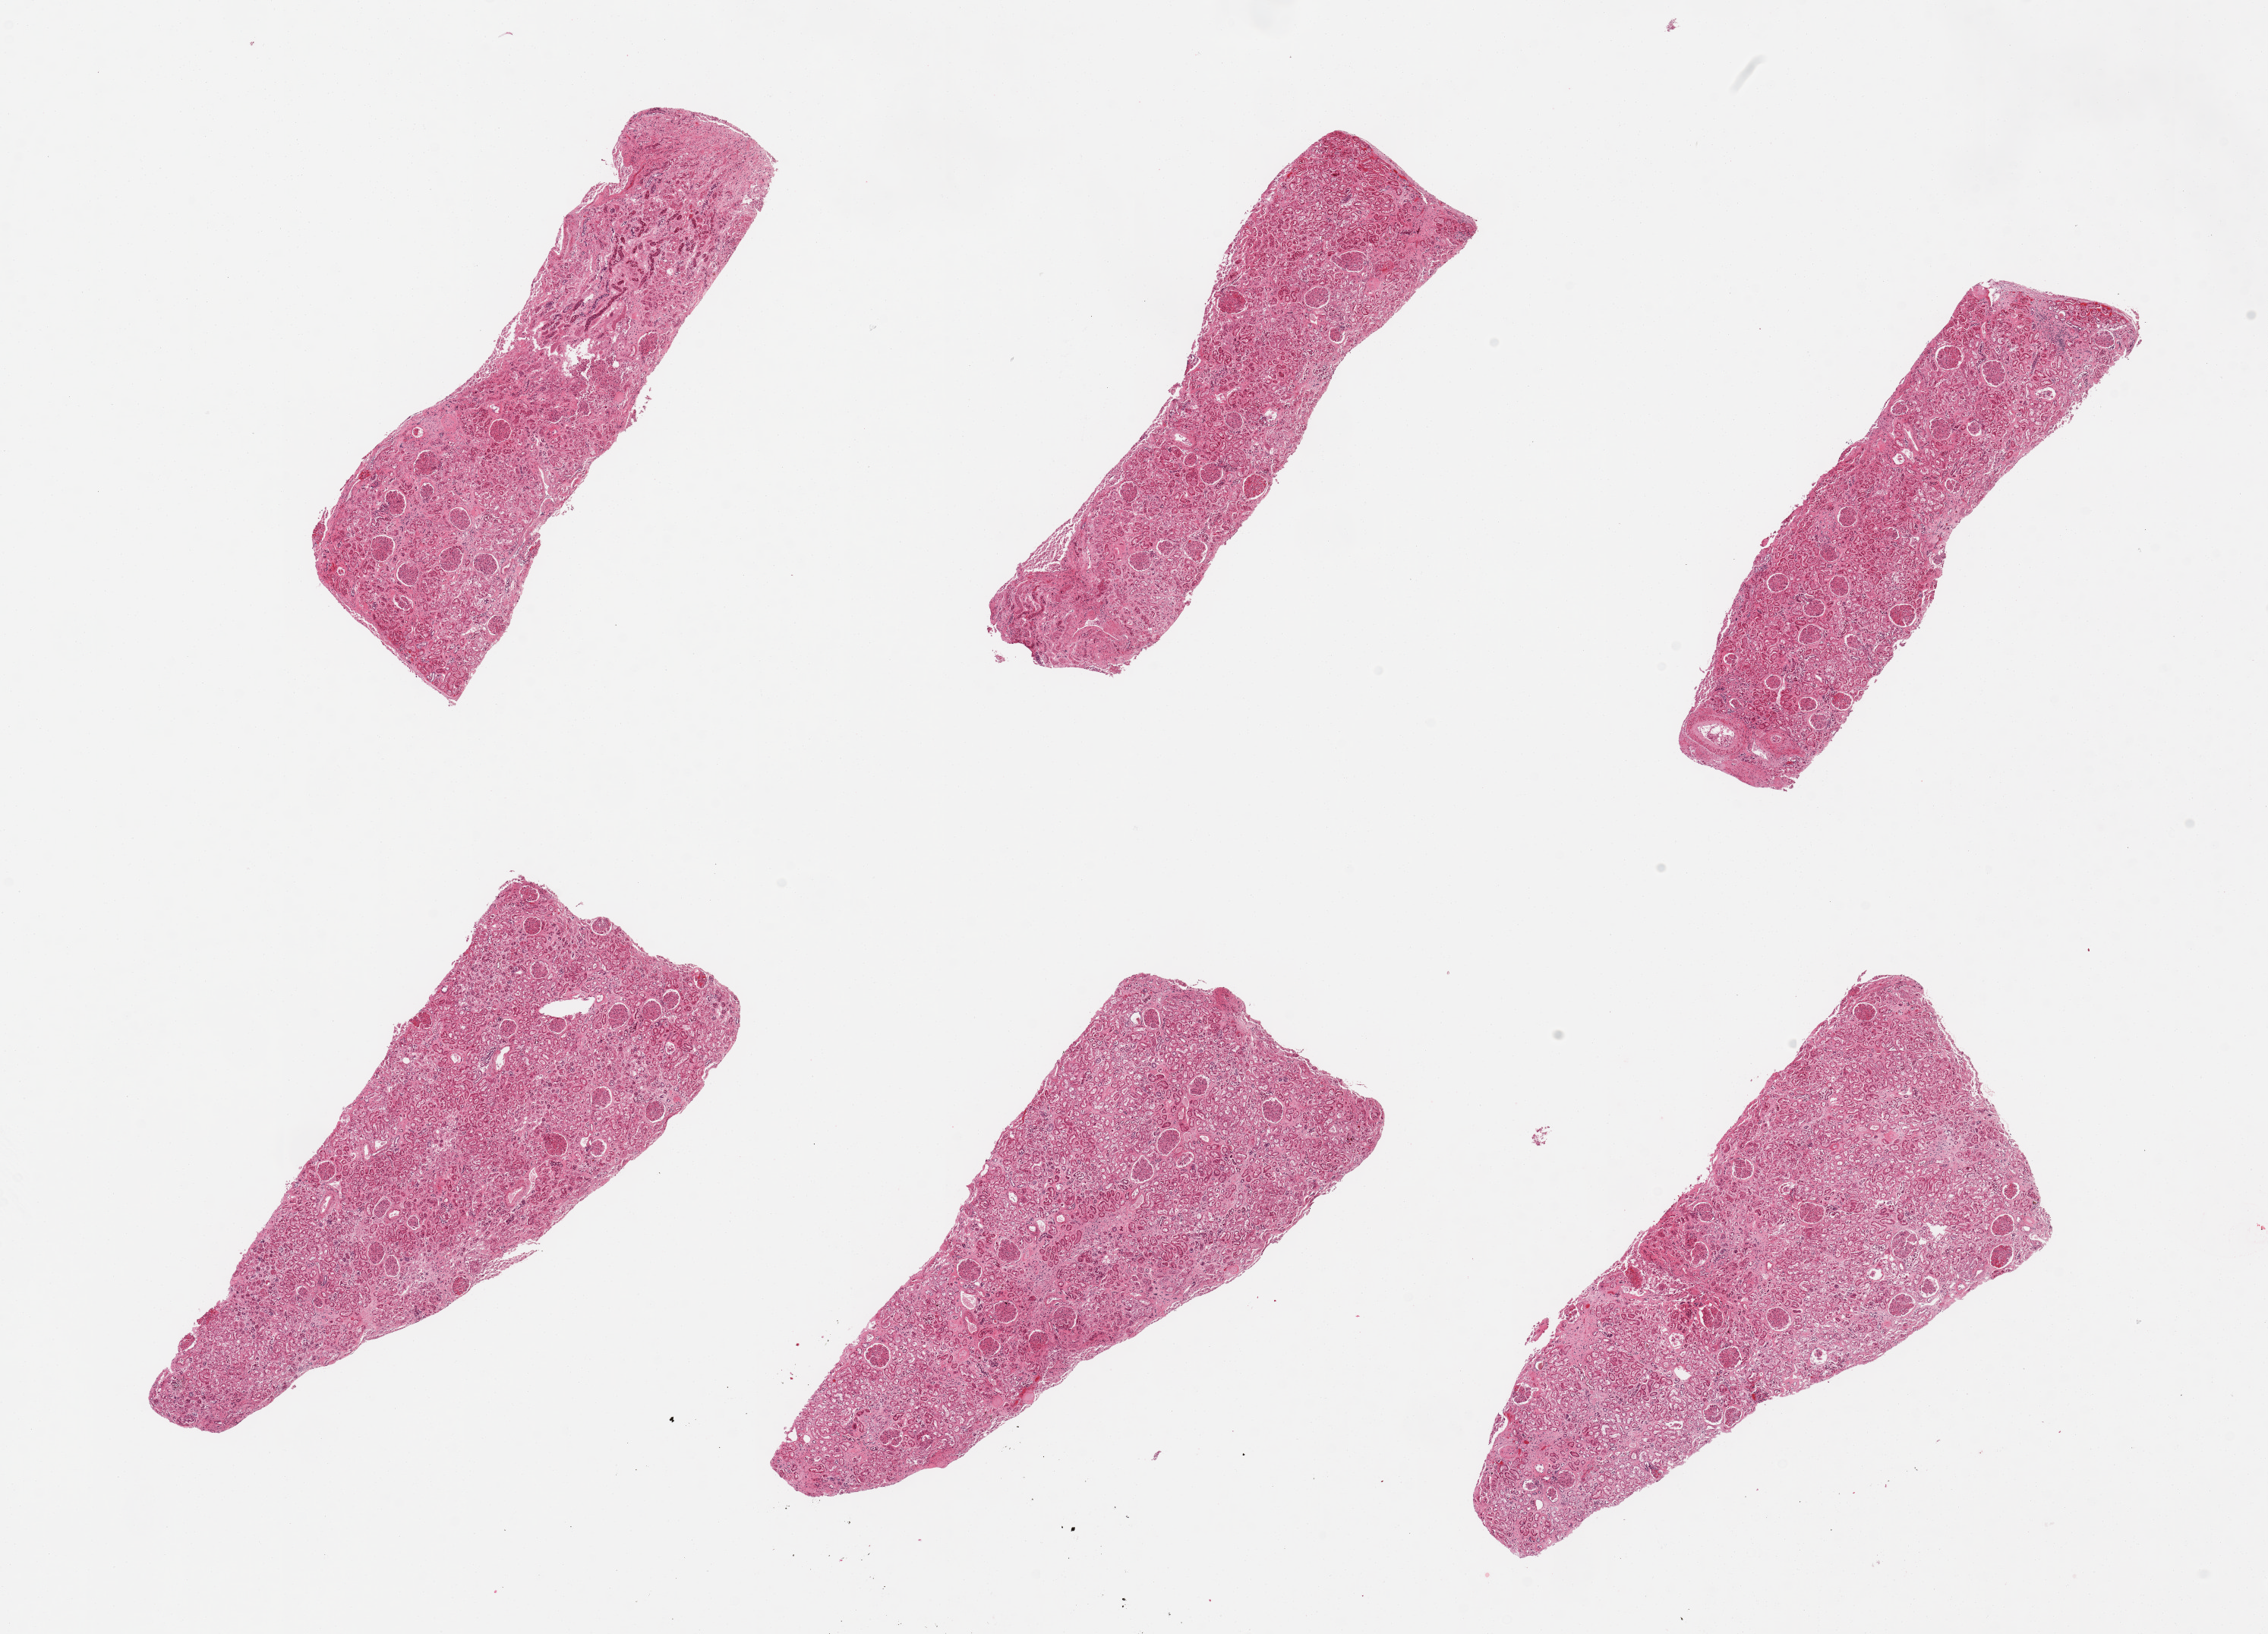
H&E whole-slide image, brightfield — shown as a low-resolution overview of the whole scanned area (about 23.6 x 17.0 mm, acquisition: 20x scan), PAXgene-fixed paraffin-embedded (PFPE) section, target tissue: renal cortex, tissue donor sample. Male donor.
Review note (as recorded): 6 pieces; interstitial fibrosis, occasional sclerotic glomeruli, arteriolosclerosis.